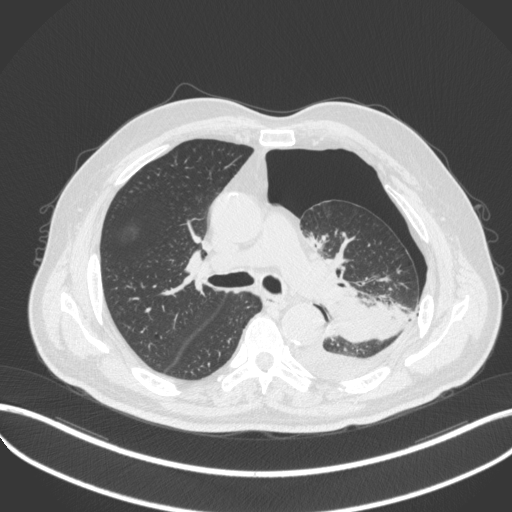
Chest CT, one axial slice; slice 323 of 466 in the series (ordered by position); 120 kVp; lung window (W 1500 / L -600 HU); 1 mm slice thickness; 512 × 512 image matrix. Patient: male, 76 years. Case-level facts recorded for this patient, not image findings: clinical TNM (as recorded): T3 N0 M1b.
Outlined on this slice (rectangle marked by the reading radiologist):
- lung tumour (recorded histology: adenocarcinoma): bounding box [x1, y1, x2, y2] px = [319, 286, 406, 345]